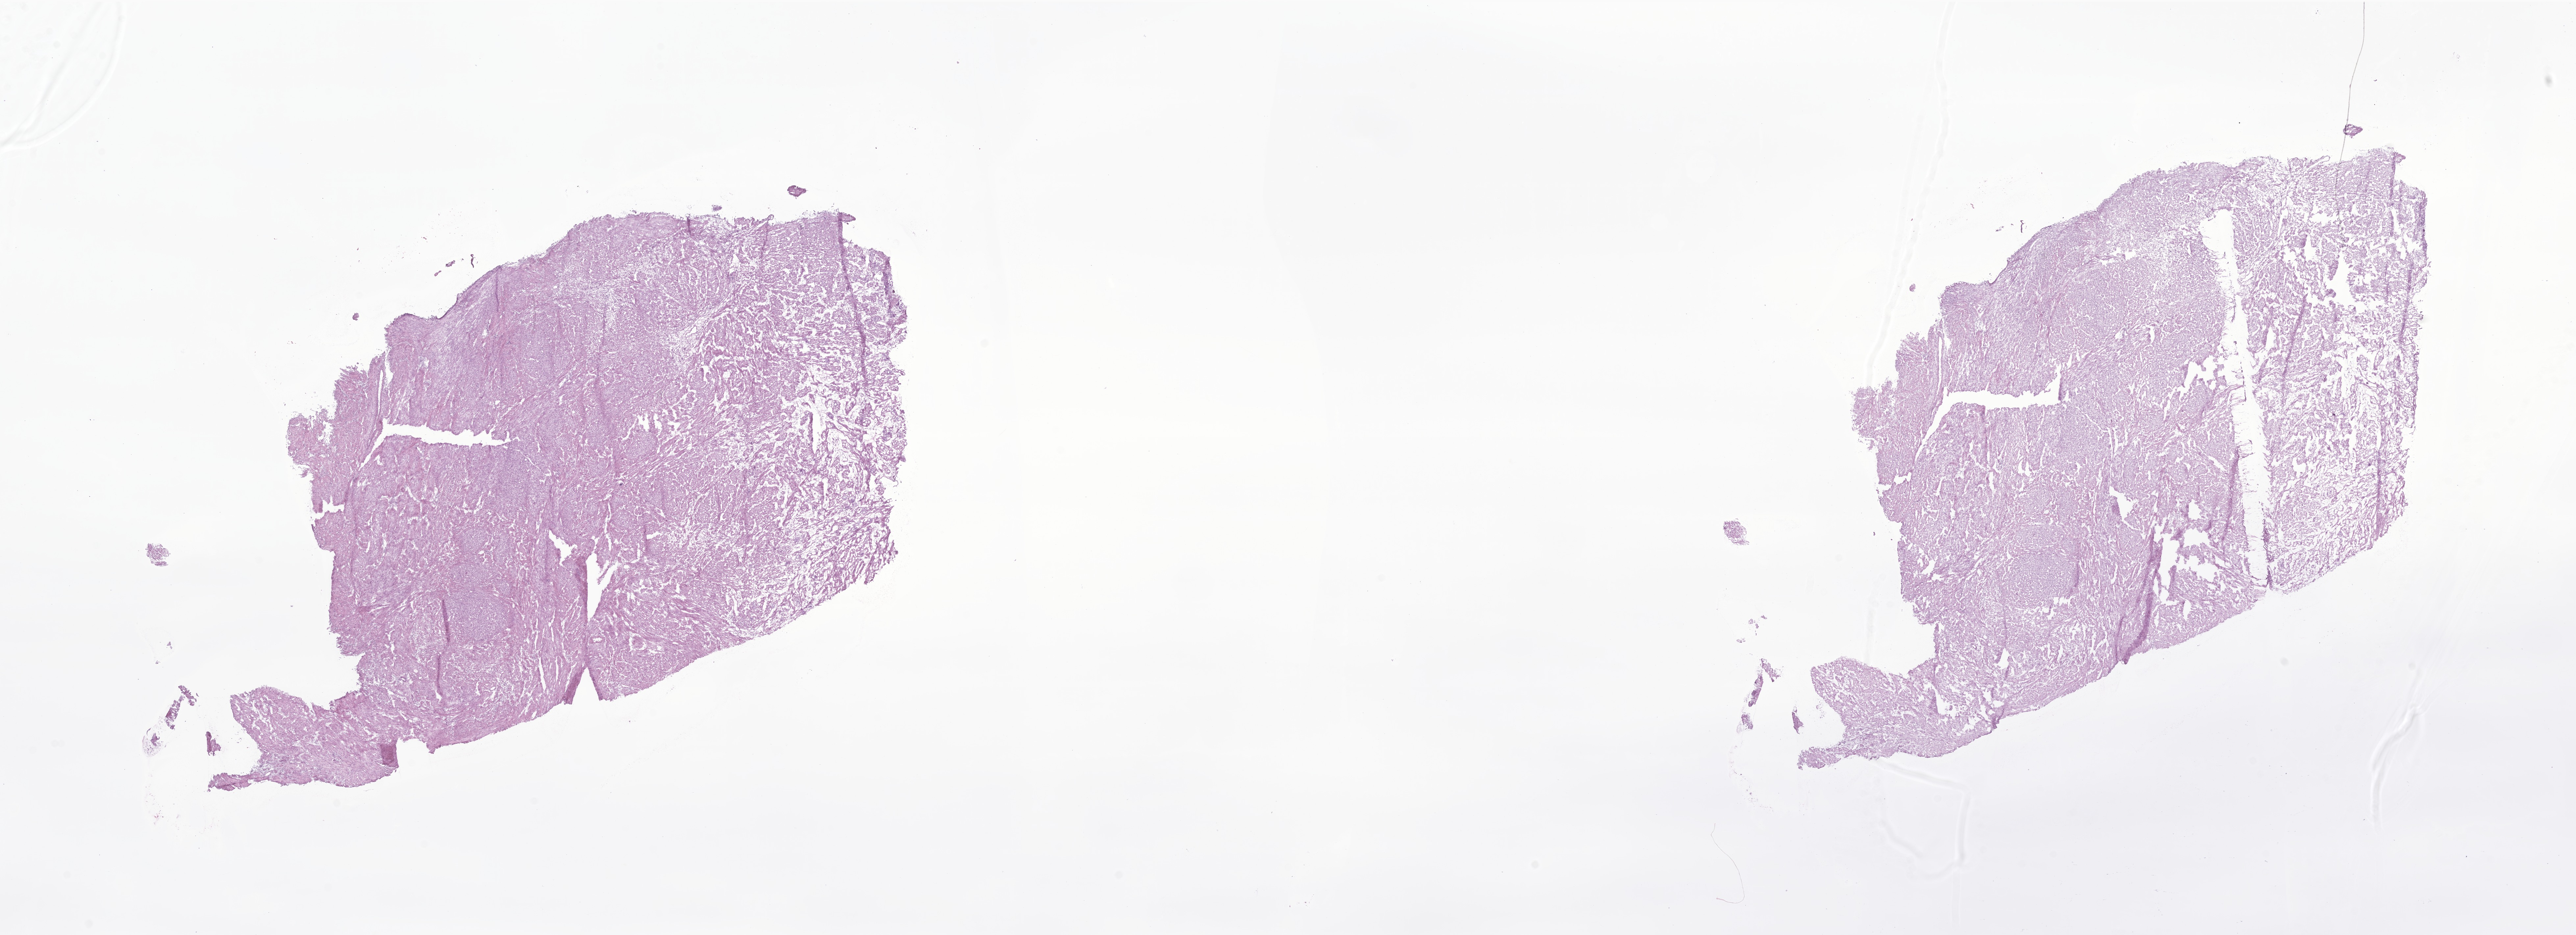
Whole-slide image, hematoxylin and eosin (H&E) stain of tumor tissue from the posterior mediastinum, whole scanned area (about 33.0 x 12.0 mm) shown as a low-resolution overview. Cryosection (OCT / tissue freezing medium). Patient female; age 79 months (6 years 7 months).
Diagnosis (ICD-O-3 morphology term): Ganglioneuroblastoma.